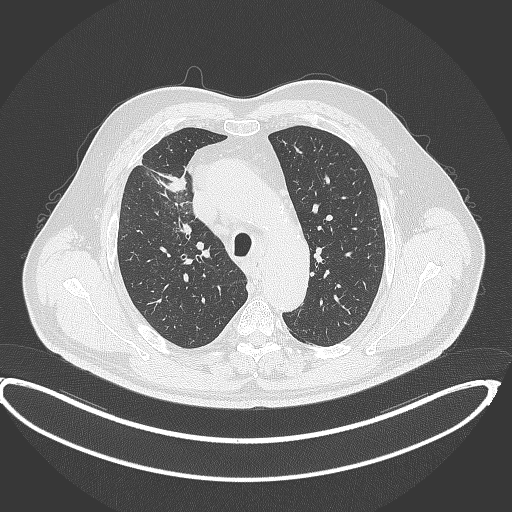
Chest CT, one axial slice; position 302 of 390 along the scan axis; reconstruction kernel B70f; 120 kVp; lung window (W 1500 / L -600 HU); 1 mm slice thickness; 512 × 512 image matrix. Male patient, age 62 years. From the clinical record (not read from this slice): clinical TNM (as recorded): T1c N3 M1c.
Outlined on this slice (bounding box drawn by a radiologist):
- lung tumour (recorded histology: adenocarcinoma): bounding box [x1, y1, x2, y2] px = [163, 170, 188, 193]